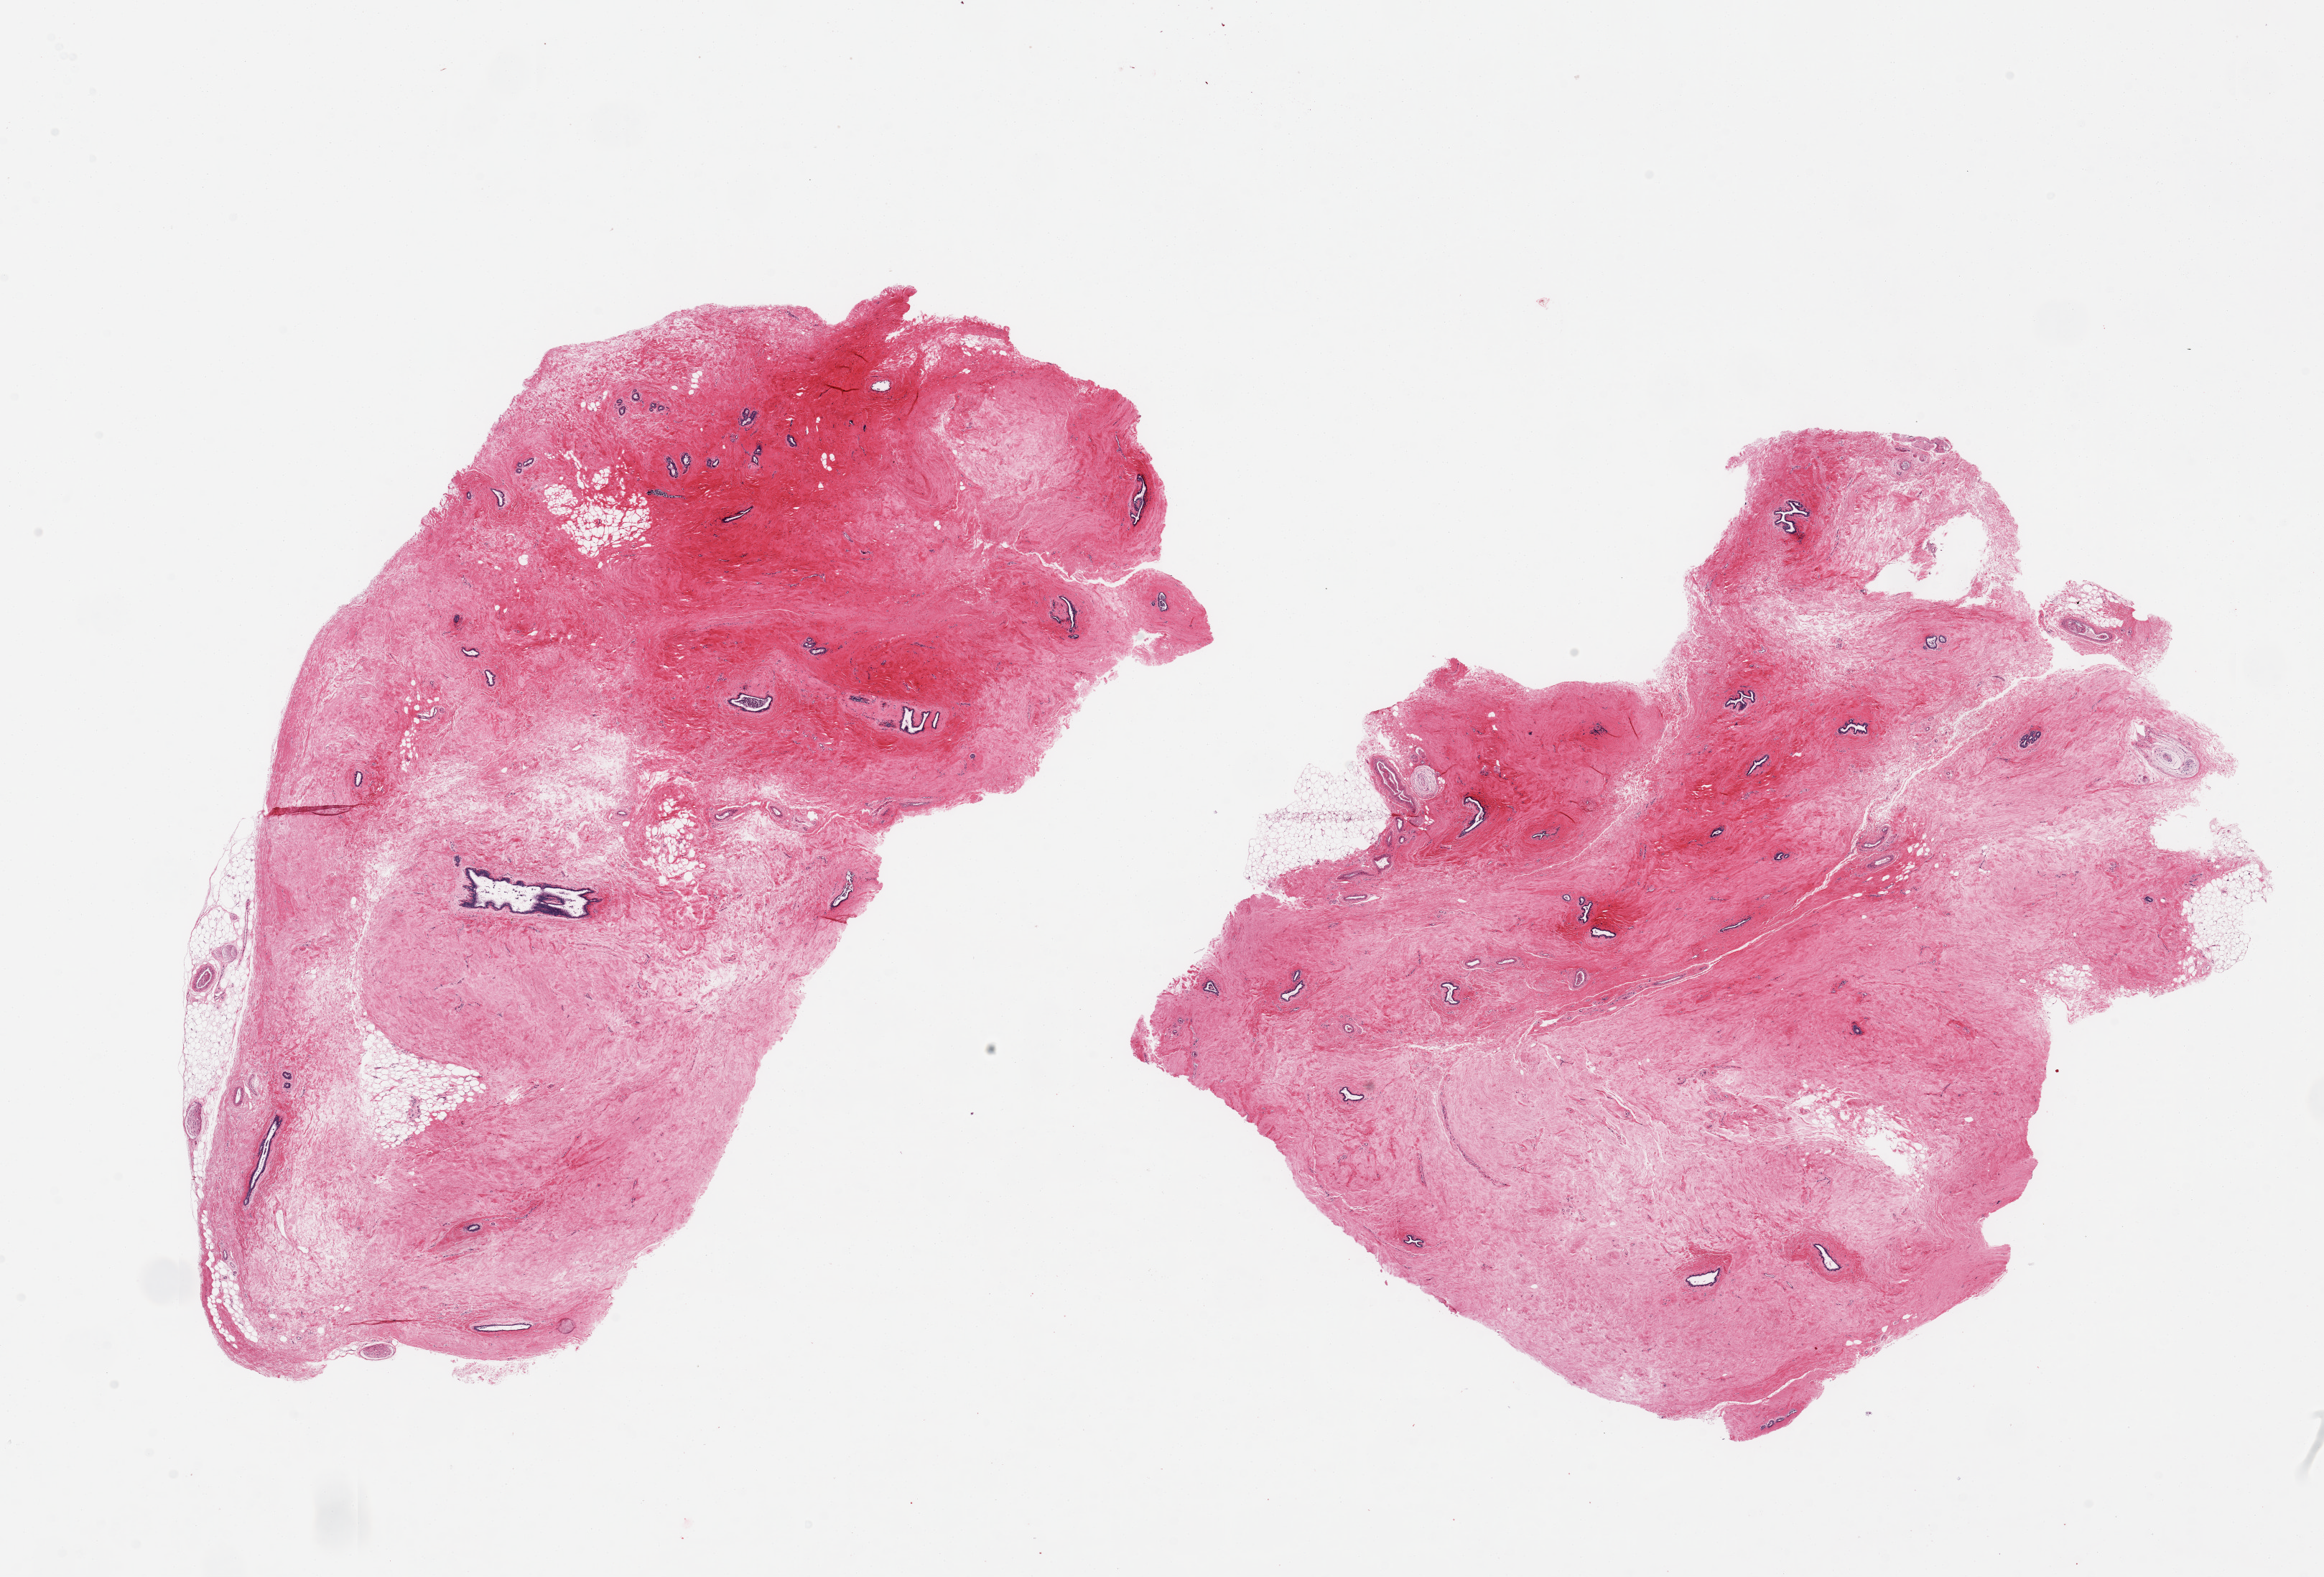
Whole-slide image, haematoxylin and eosin stain, shown as a low-resolution overview of the whole scanned area (about 25.6 x 17.4 mm, from a 20x scan); PAXgene-fixed, paraffin-embedded tissue; target tissue: breast; tissue donor sample.
Pathologist's review note for this sample: 2 pieces; fibrous stroma with mammary ducts: gynecomastoid change.